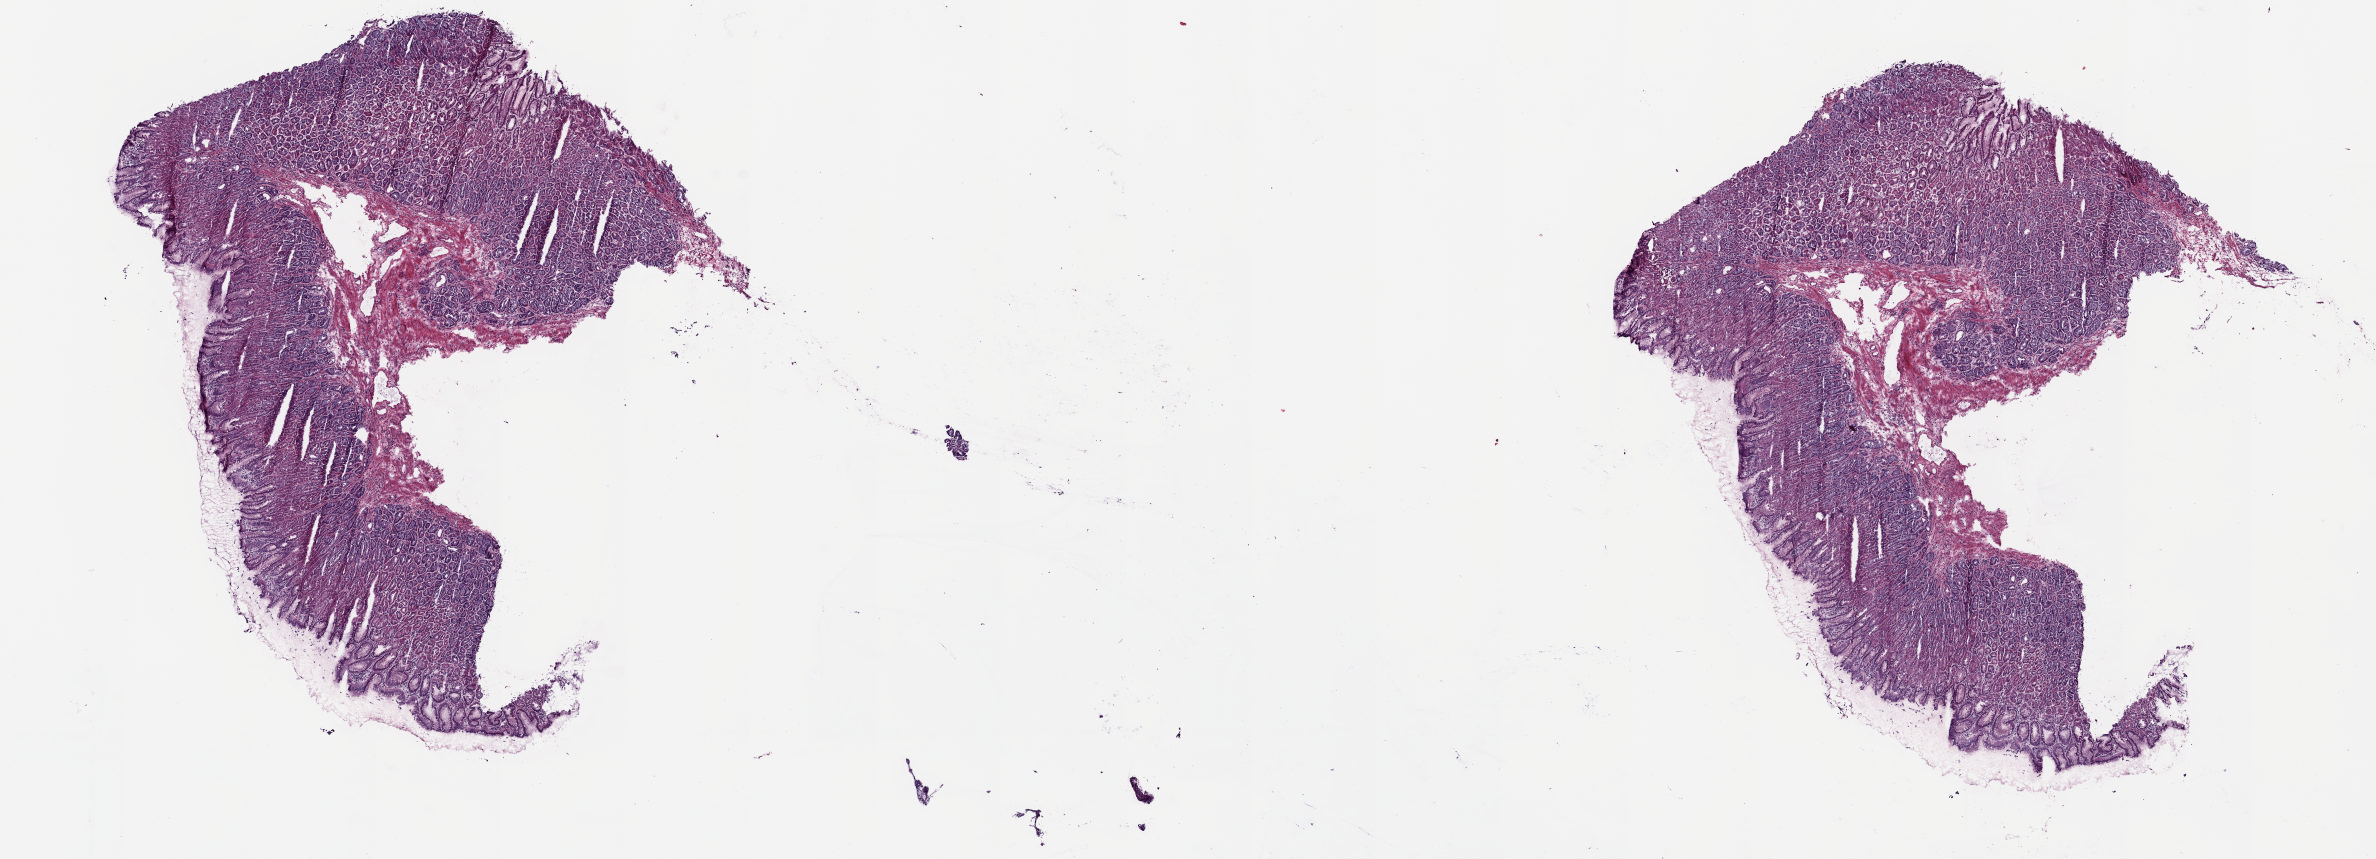
H&E-stained whole-slide image, whole scanned area (about 18.8 x 6.8 mm, acquisition: 20x scan) shown as a low-resolution overview; frozen section from the top of the tissue portion; sample: solid tissue normal (non-tumour tissue), esophagus. Male, age 83 years at initial diagnosis. Slide review estimates, as recorded: tumour cells 0%, tumour nuclei 0%, normal cells 100%, stromal cells 0%, necrosis 0%. Inflammatory infiltration, as recorded: lymphocyte infiltration 3%, monocyte infiltration 0%, neutrophil infiltration 0%.
This section: solid tissue normal (non-tumour) sample from the same patient. Patient diagnosis: Adenocarcinoma, NOS.